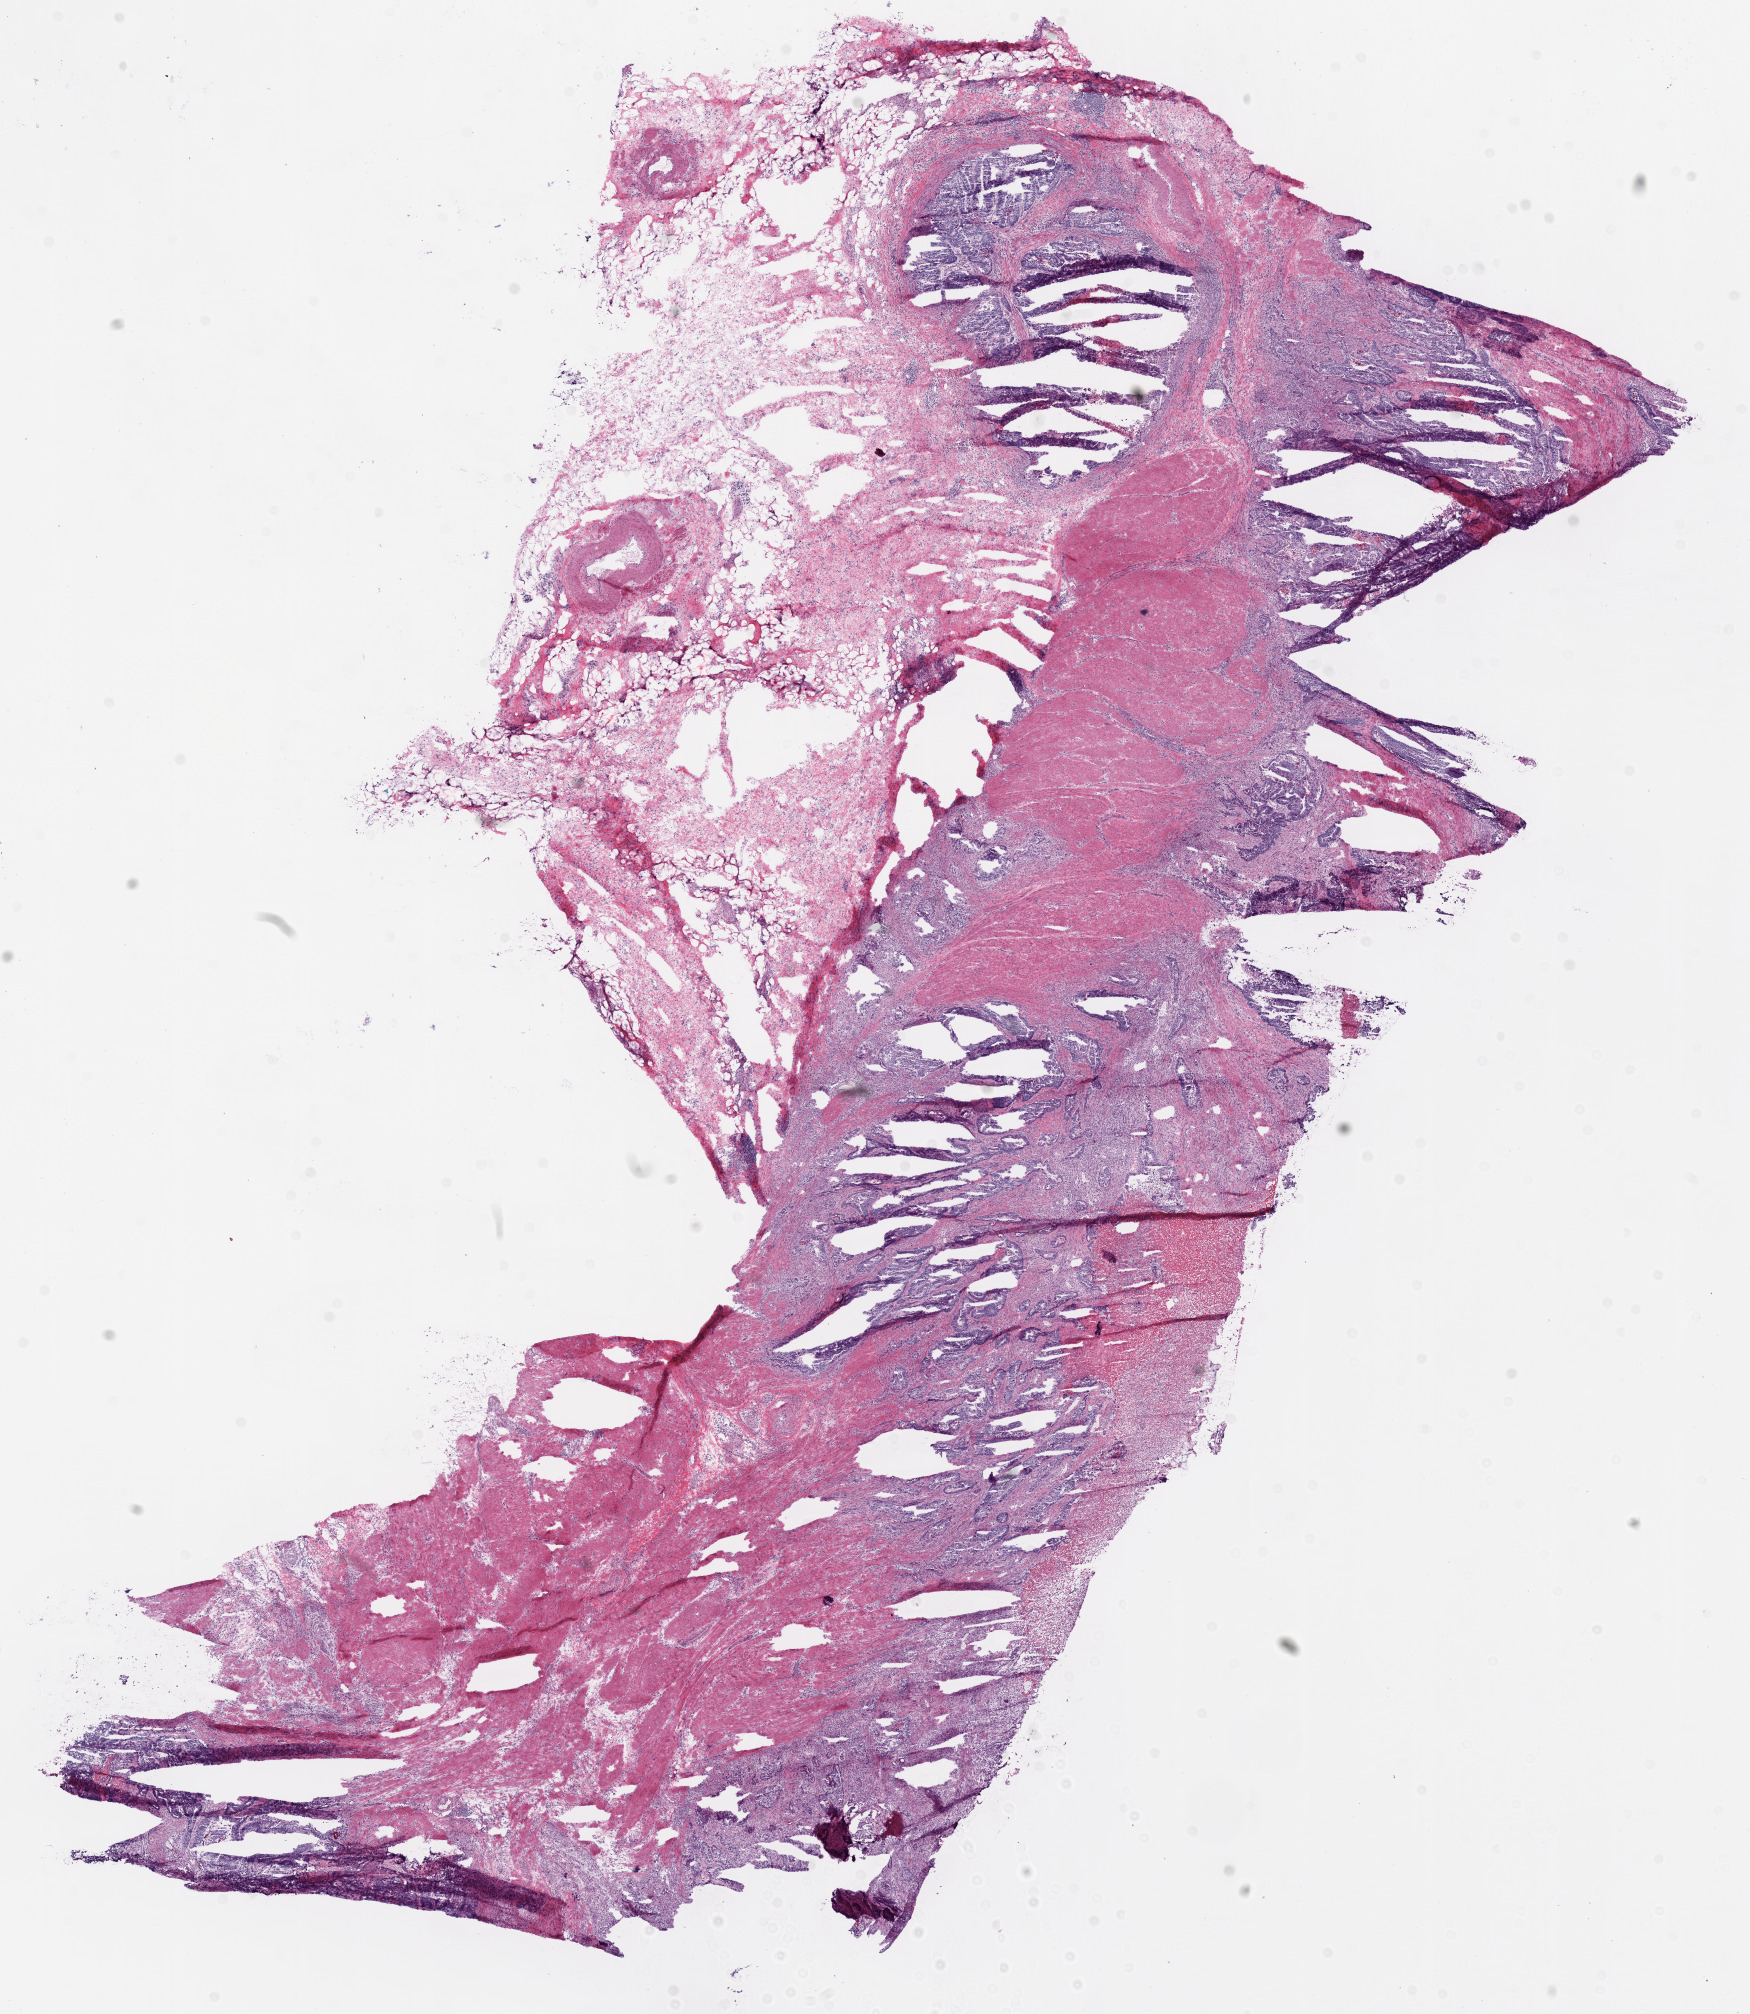
Digitized H&E-stained tissue section (whole slide), shown as a low-resolution overview of the whole scanned area (about 14.0 x 16.2 mm), frozen section, sample: primary tumour, rectum. Patient: male, age at initial diagnosis 57 years. Pathologist review of this section (percent, as recorded): tumour cells 45%, tumour nuclei 70%, normal cells 40%, stromal cells 5%, necrosis 10%.
- AJCC pathologic stage: IIIC
- histologic diagnosis: Adenocarcinoma, NOS
- lymph nodes positive (case pathology): 6 of 16 examined